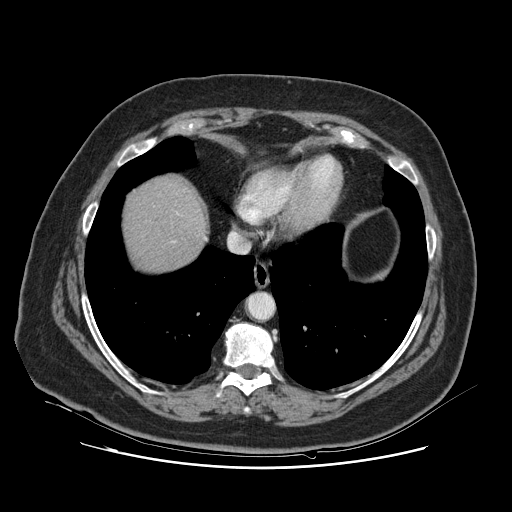
Contrast-enhanced abdominal CT, one axial slice; position 114 of 132 along the scan axis; 120 kVp; intravenous contrast given; soft-tissue window (W 400 / L 40 HU); 2.5 mm slice thickness; 512 × 512 image matrix, field of view 391 × 391 mm. Female patient, age 73 years. From the clinical record (not read from this slice): diagnosis: colorectal cancer liver metastases, imaged before liver resection; multiple liver metastases: no; largest metastasis: 7 cm.
Annotated regions visible in this slice (manually delineated by an expert):
- liver: bounding box (x1, y1, x2, y2) in pixels: (123, 177, 205, 274)
- planned liver remnant (the part of the liver to remain after resection): (124, 177, 205, 272)